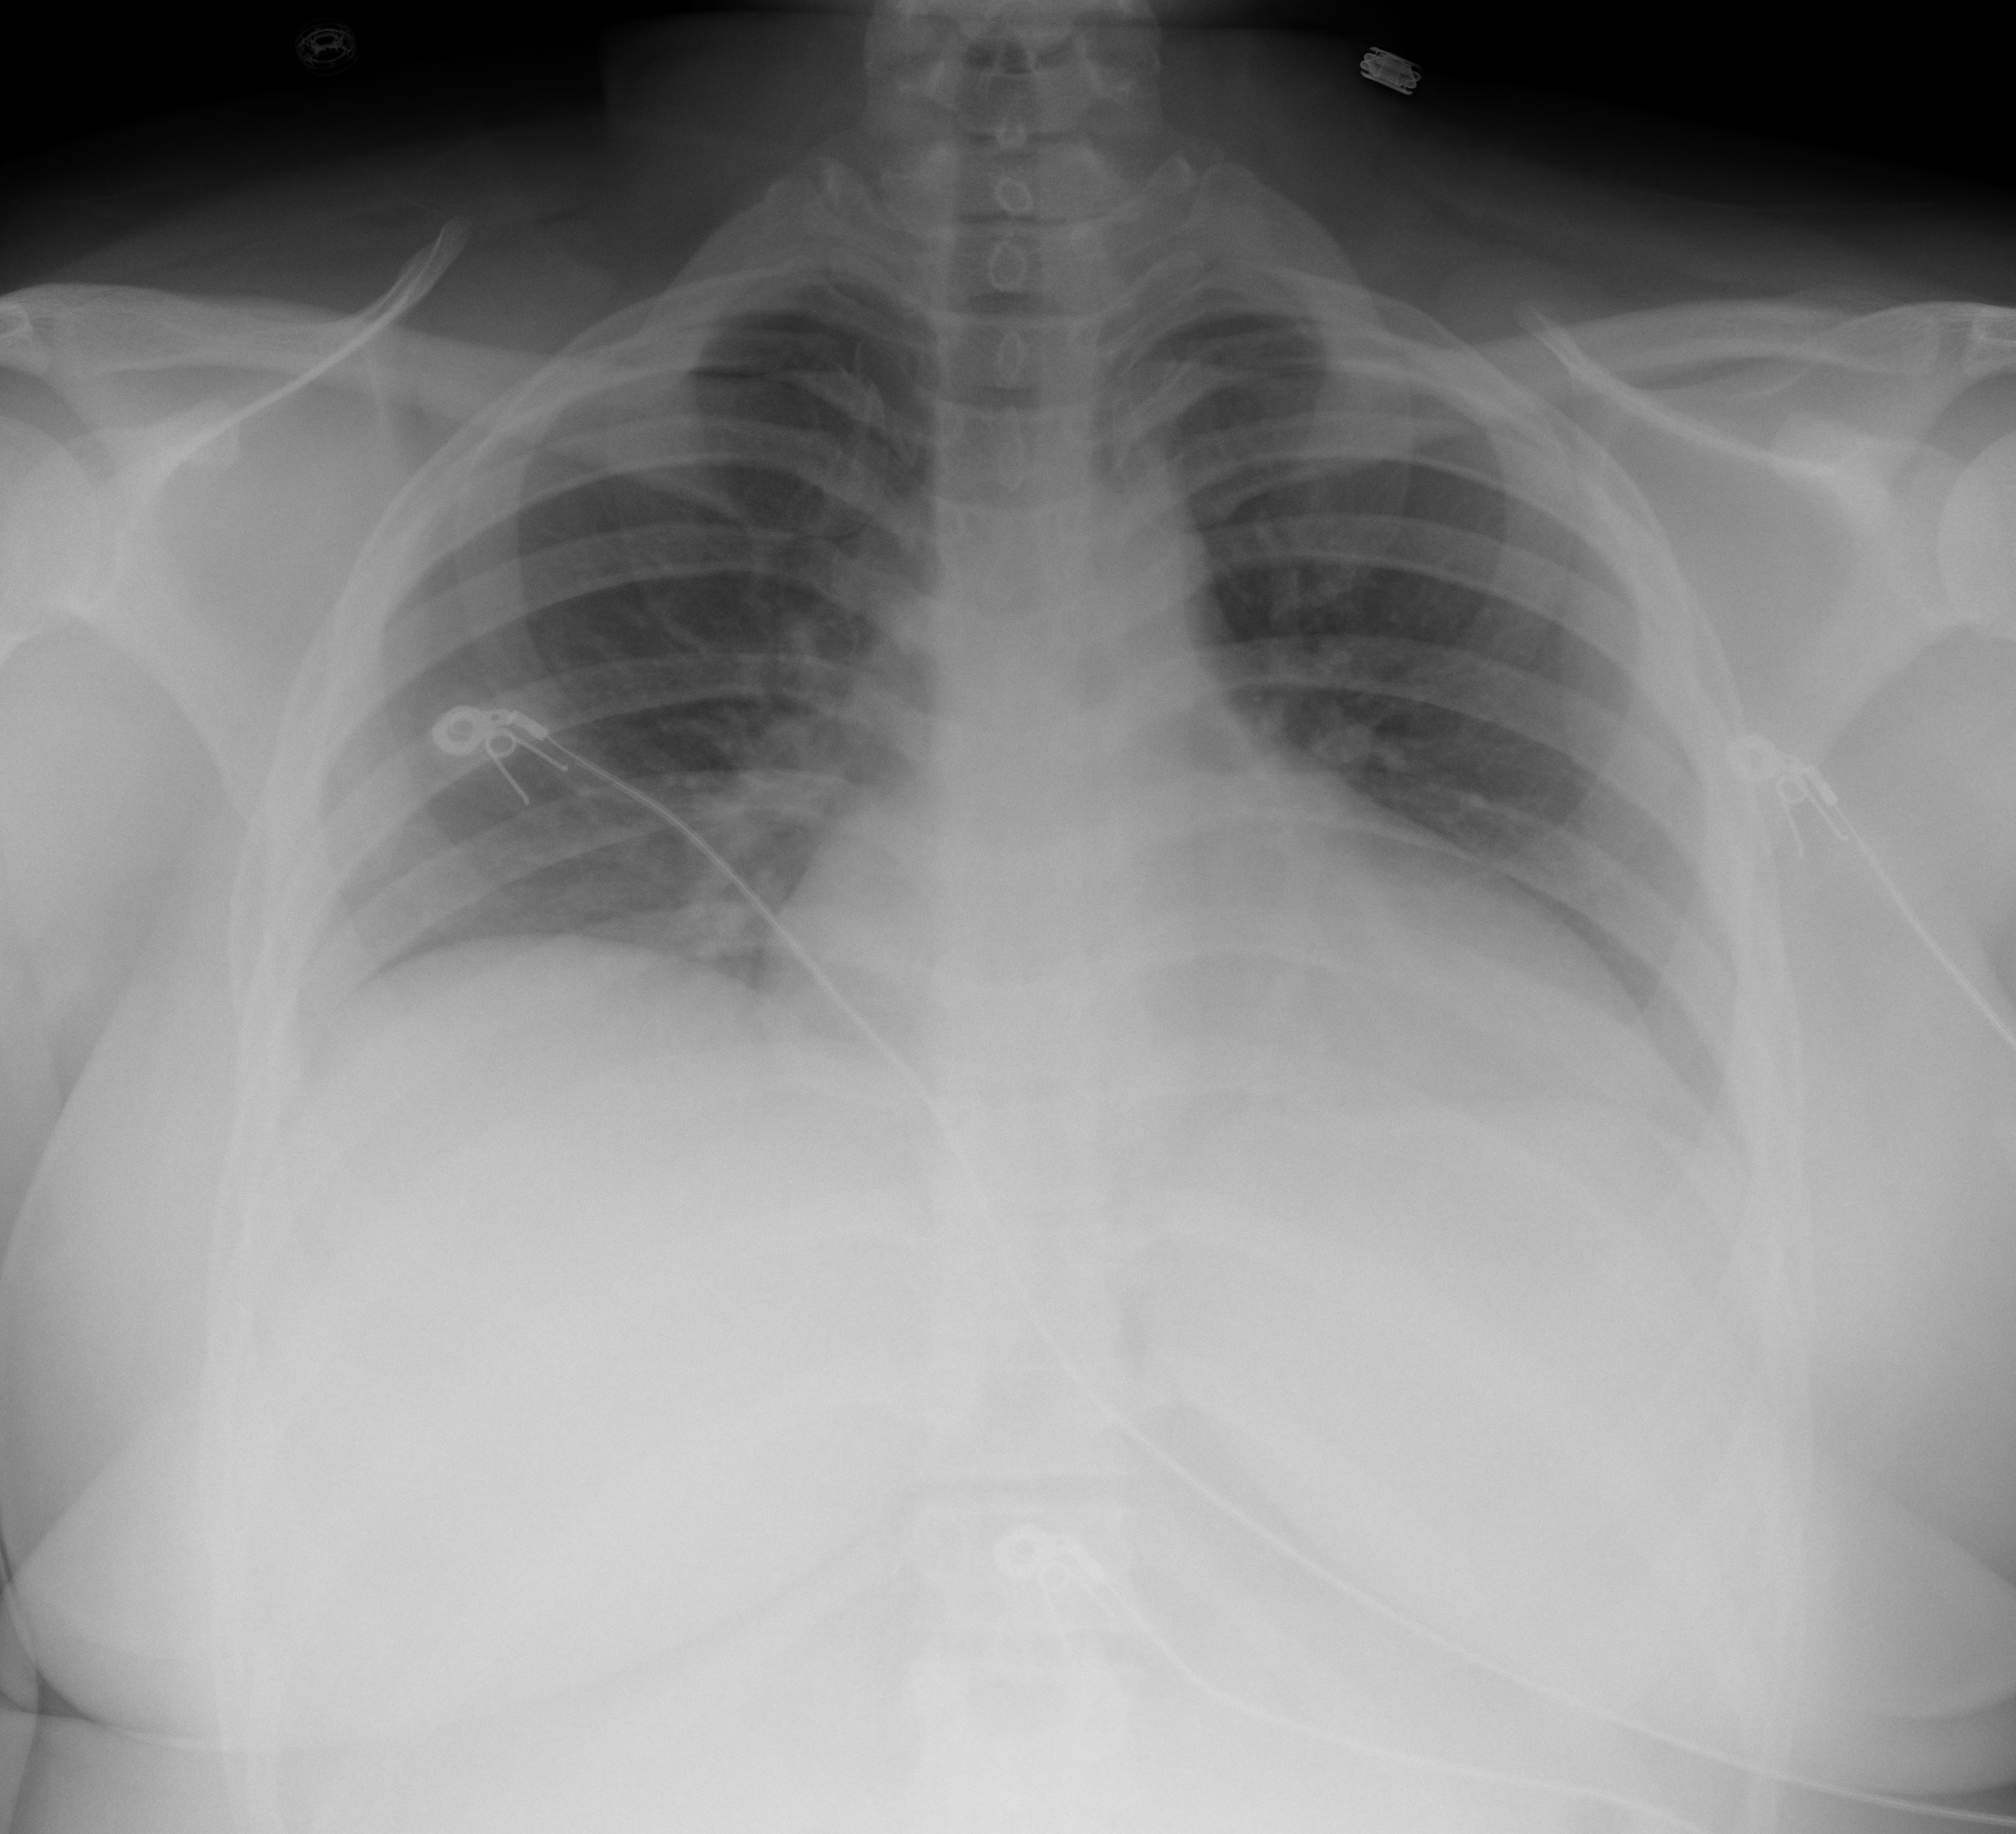
Portable chest radiograph, AP projection. Female patient, age 28 years; imaged 2 days after the COVID-19 diagnosis.
Key findings recorded by the radiologist: lungs appear clear without focal consolidation.